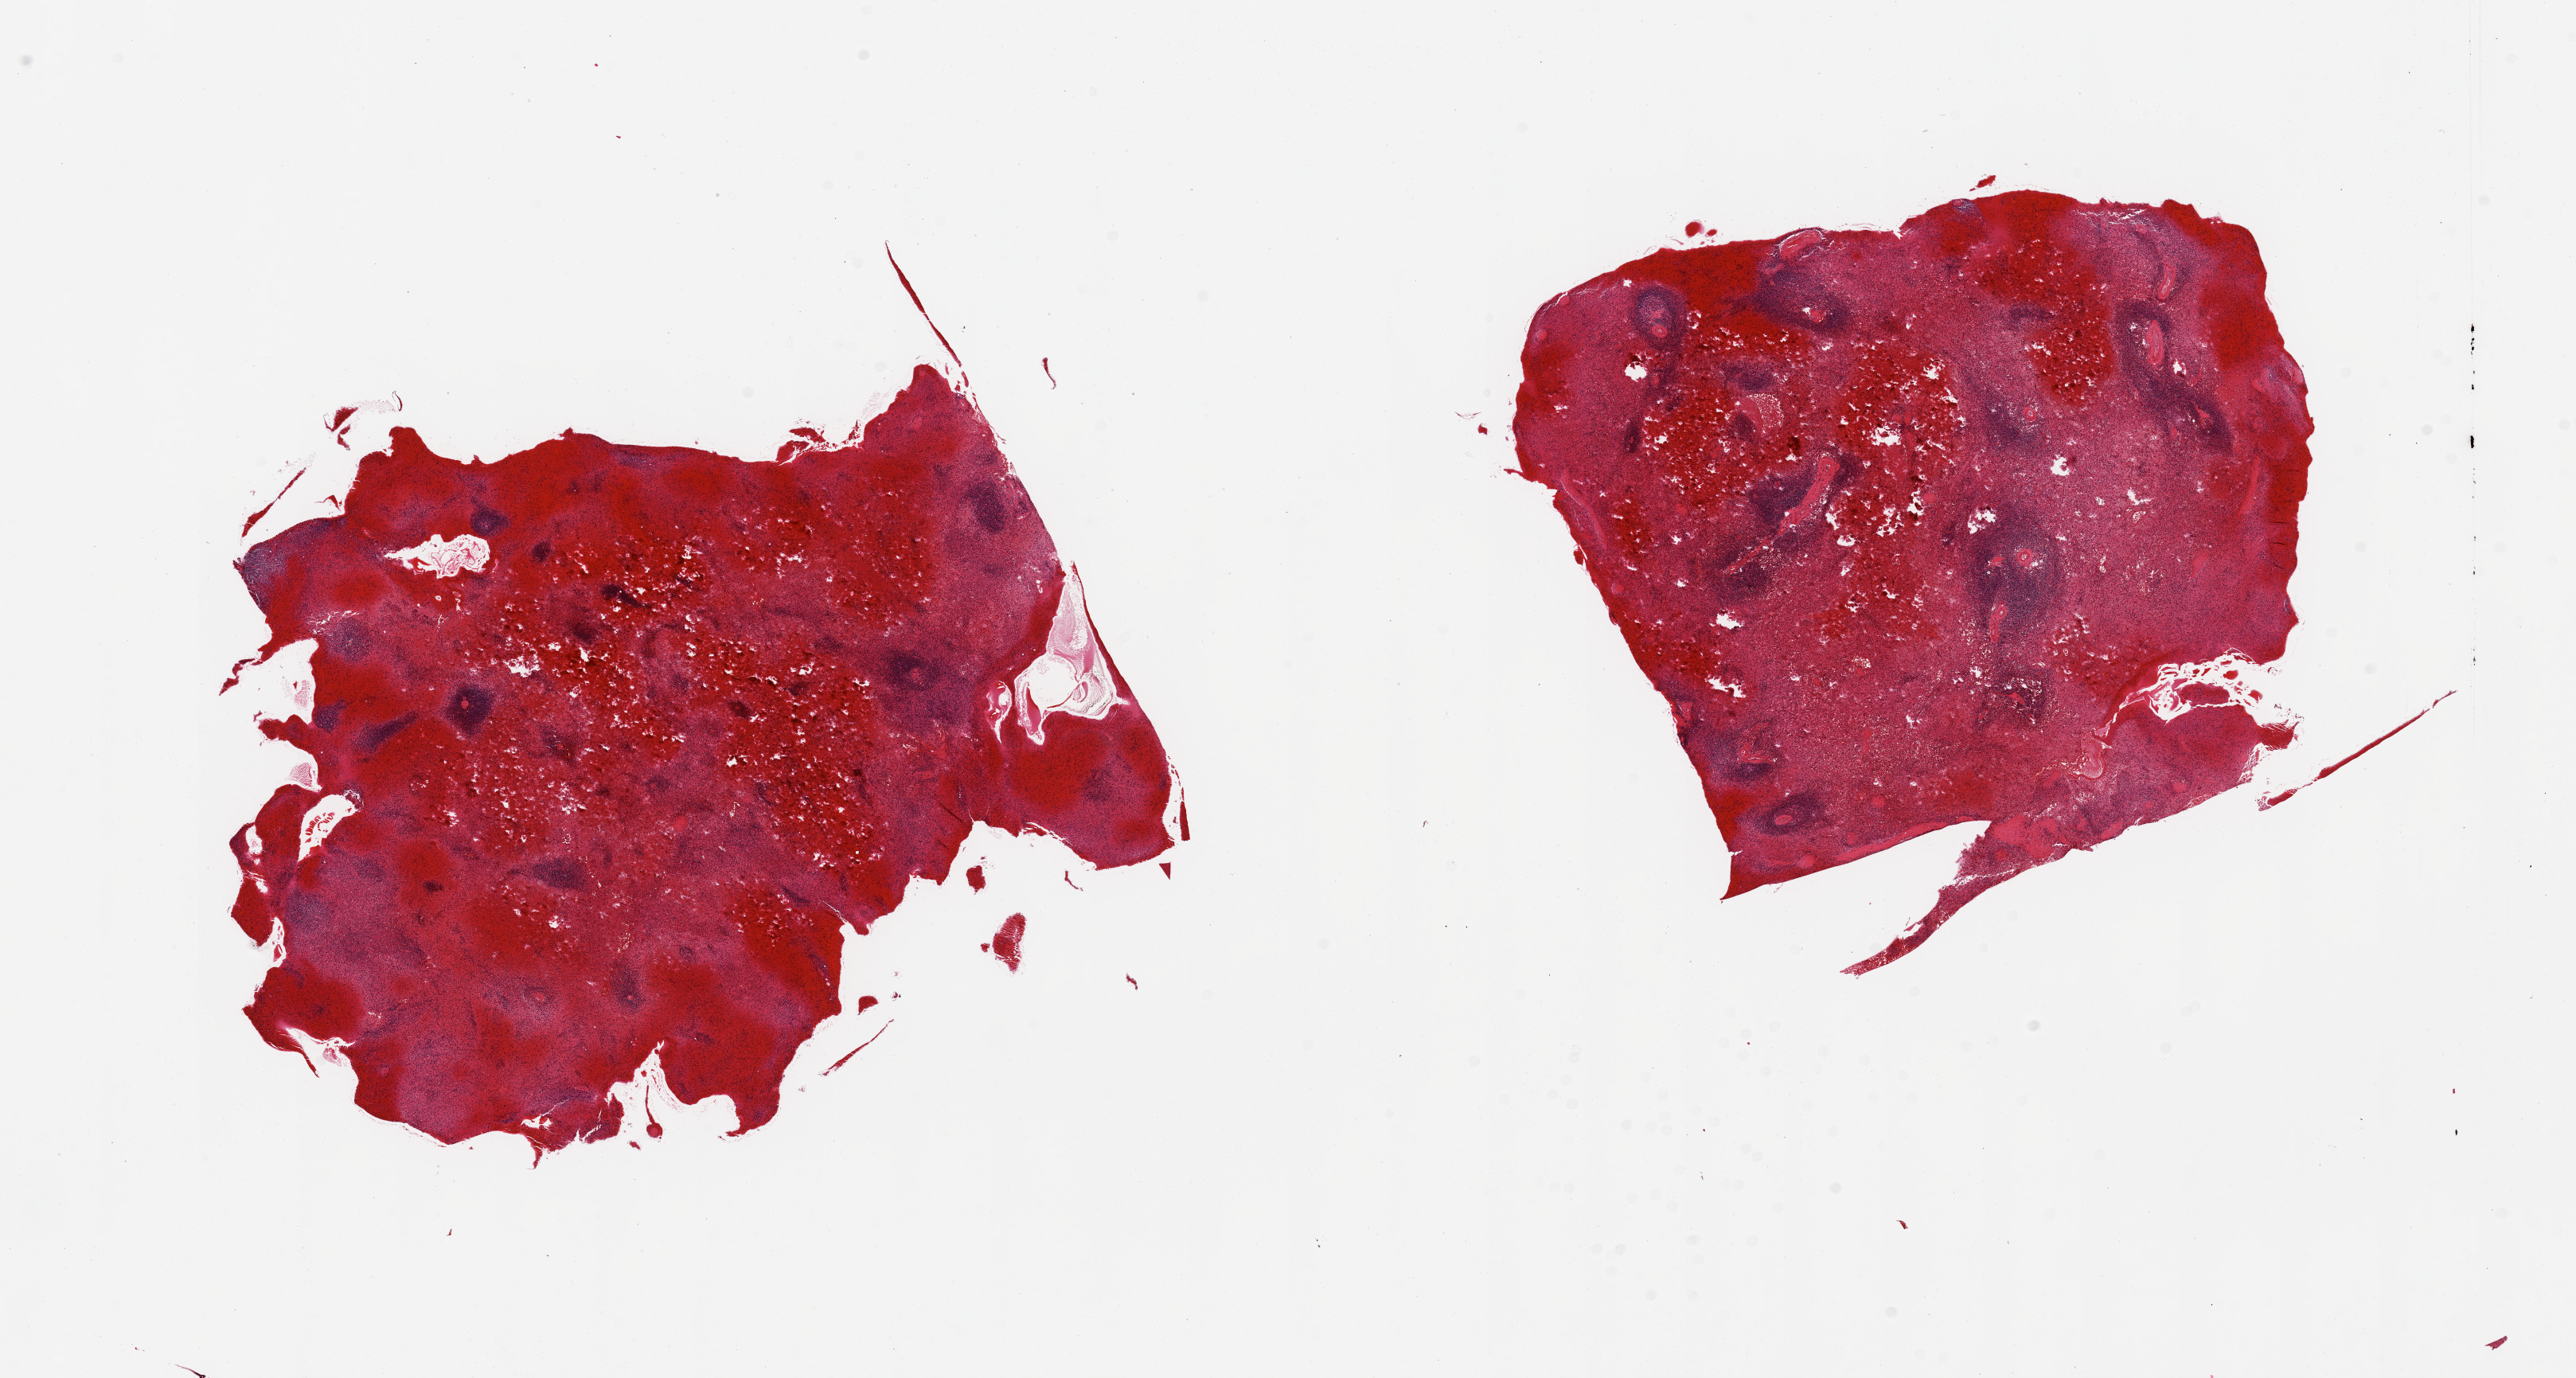
Digitized H&E-stained section — whole scanned area (about 25.6 x 13.7 mm) shown as a low-resolution overview, PAXgene-fixed, paraffin-embedded tissue, sampled site (target tissue): spleen, donor tissue sample. Donor: male.
• review note (as recorded): 2 pieces; congested